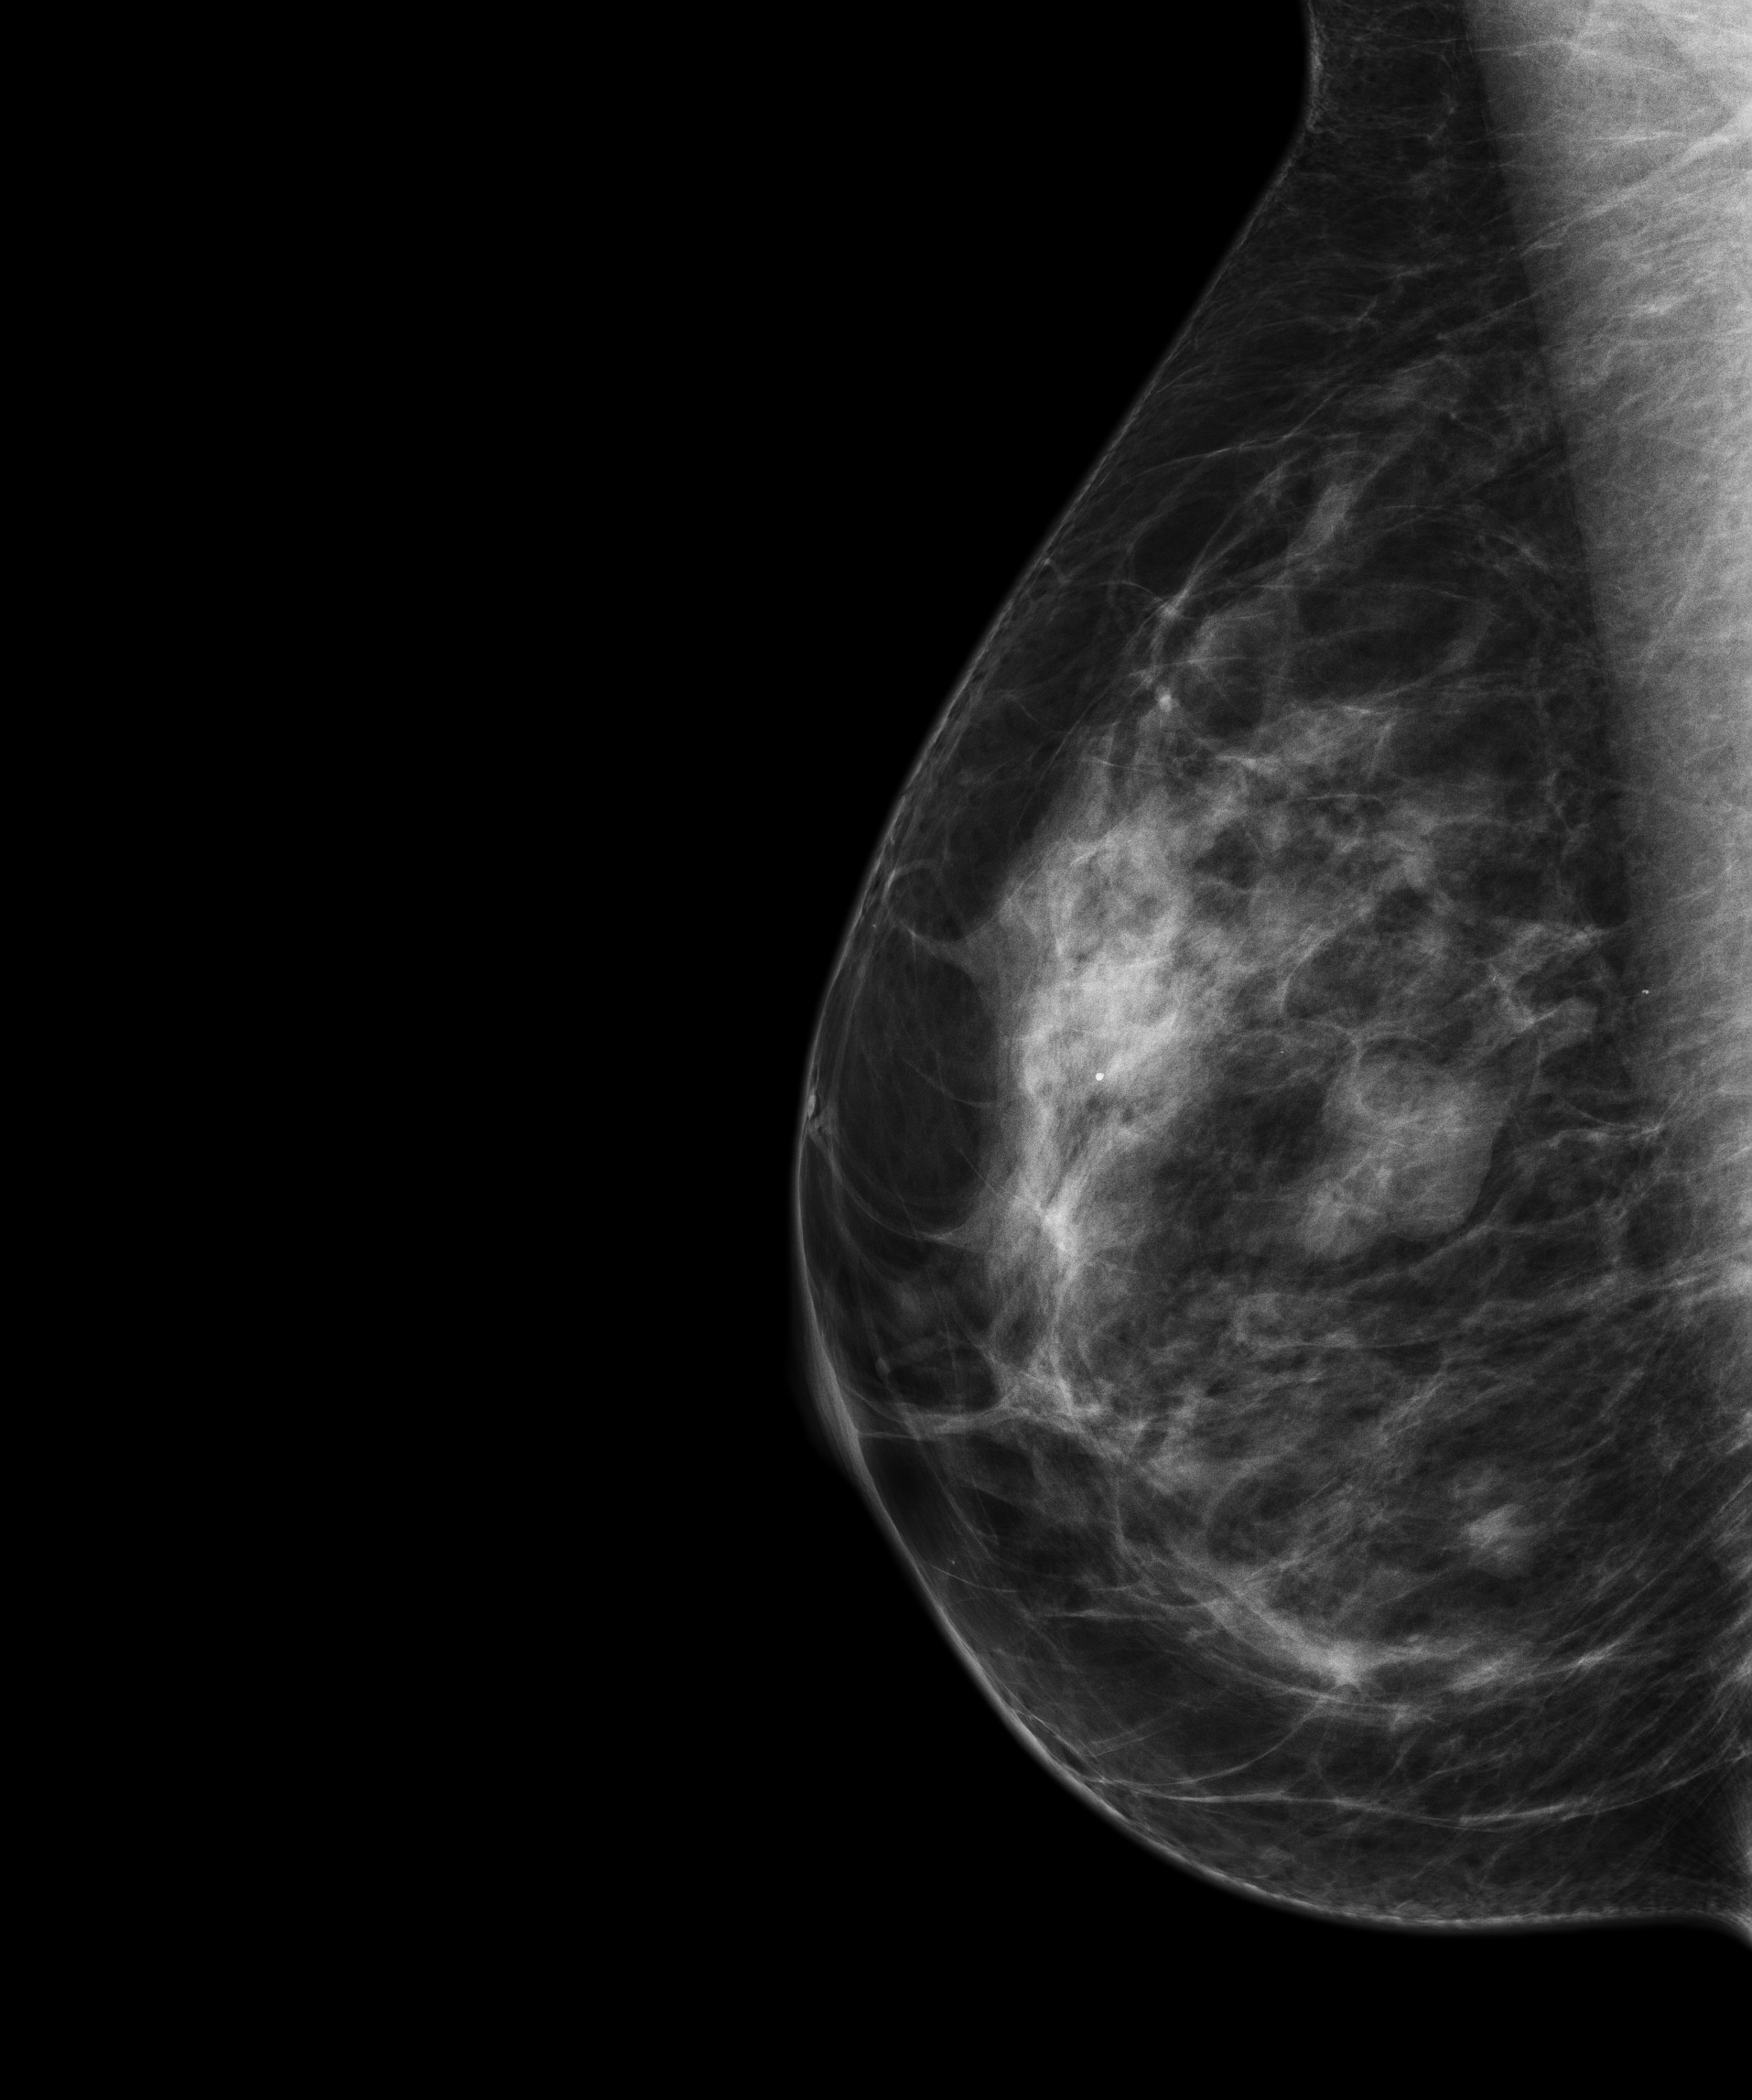
Digital mammogram (FFDM), right breast, MLO view, screening examination, compressed breast thickness 50 mm, system: Senographe Essential ADS_56.21.3. Patient aged 51 years (female).
- breast density at the screening exam (both breasts): heterogeneously dense (BI-RADS density category c)
- final BI-RADS category for the screening round (tomosynthesis exam, both breasts): category 2
- recall: no recall after this screen